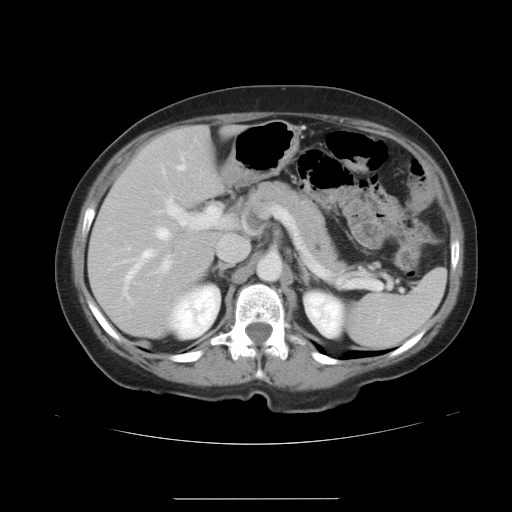
Contrast-enhanced abdominal CT, one axial slice. Position 23 of 41 along the scan axis. Intravenous contrast given. Soft-tissue window (W 400 / L 40 HU). 5 mm slice thickness. 512 × 512 image matrix, field of view 381 × 381 mm. Female patient, age 63 years. From the clinical record (not read from this slice): diagnosis: colorectal cancer liver metastases, imaged before liver resection; multiple liver metastases: yes; largest metastasis: 1.5 cm; disease in both lobes: yes.
Annotated regions visible in this slice (manually delineated by an expert):
- hepatic veins: bounding box [x1, y1, x2, y2] px = [124, 165, 185, 295]
- liver: [90, 126, 234, 337]
- planned liver remnant (the part of the liver to remain after resection): [90, 126, 223, 337]
- portal vein (with intrahepatic branches): [162, 199, 223, 271]